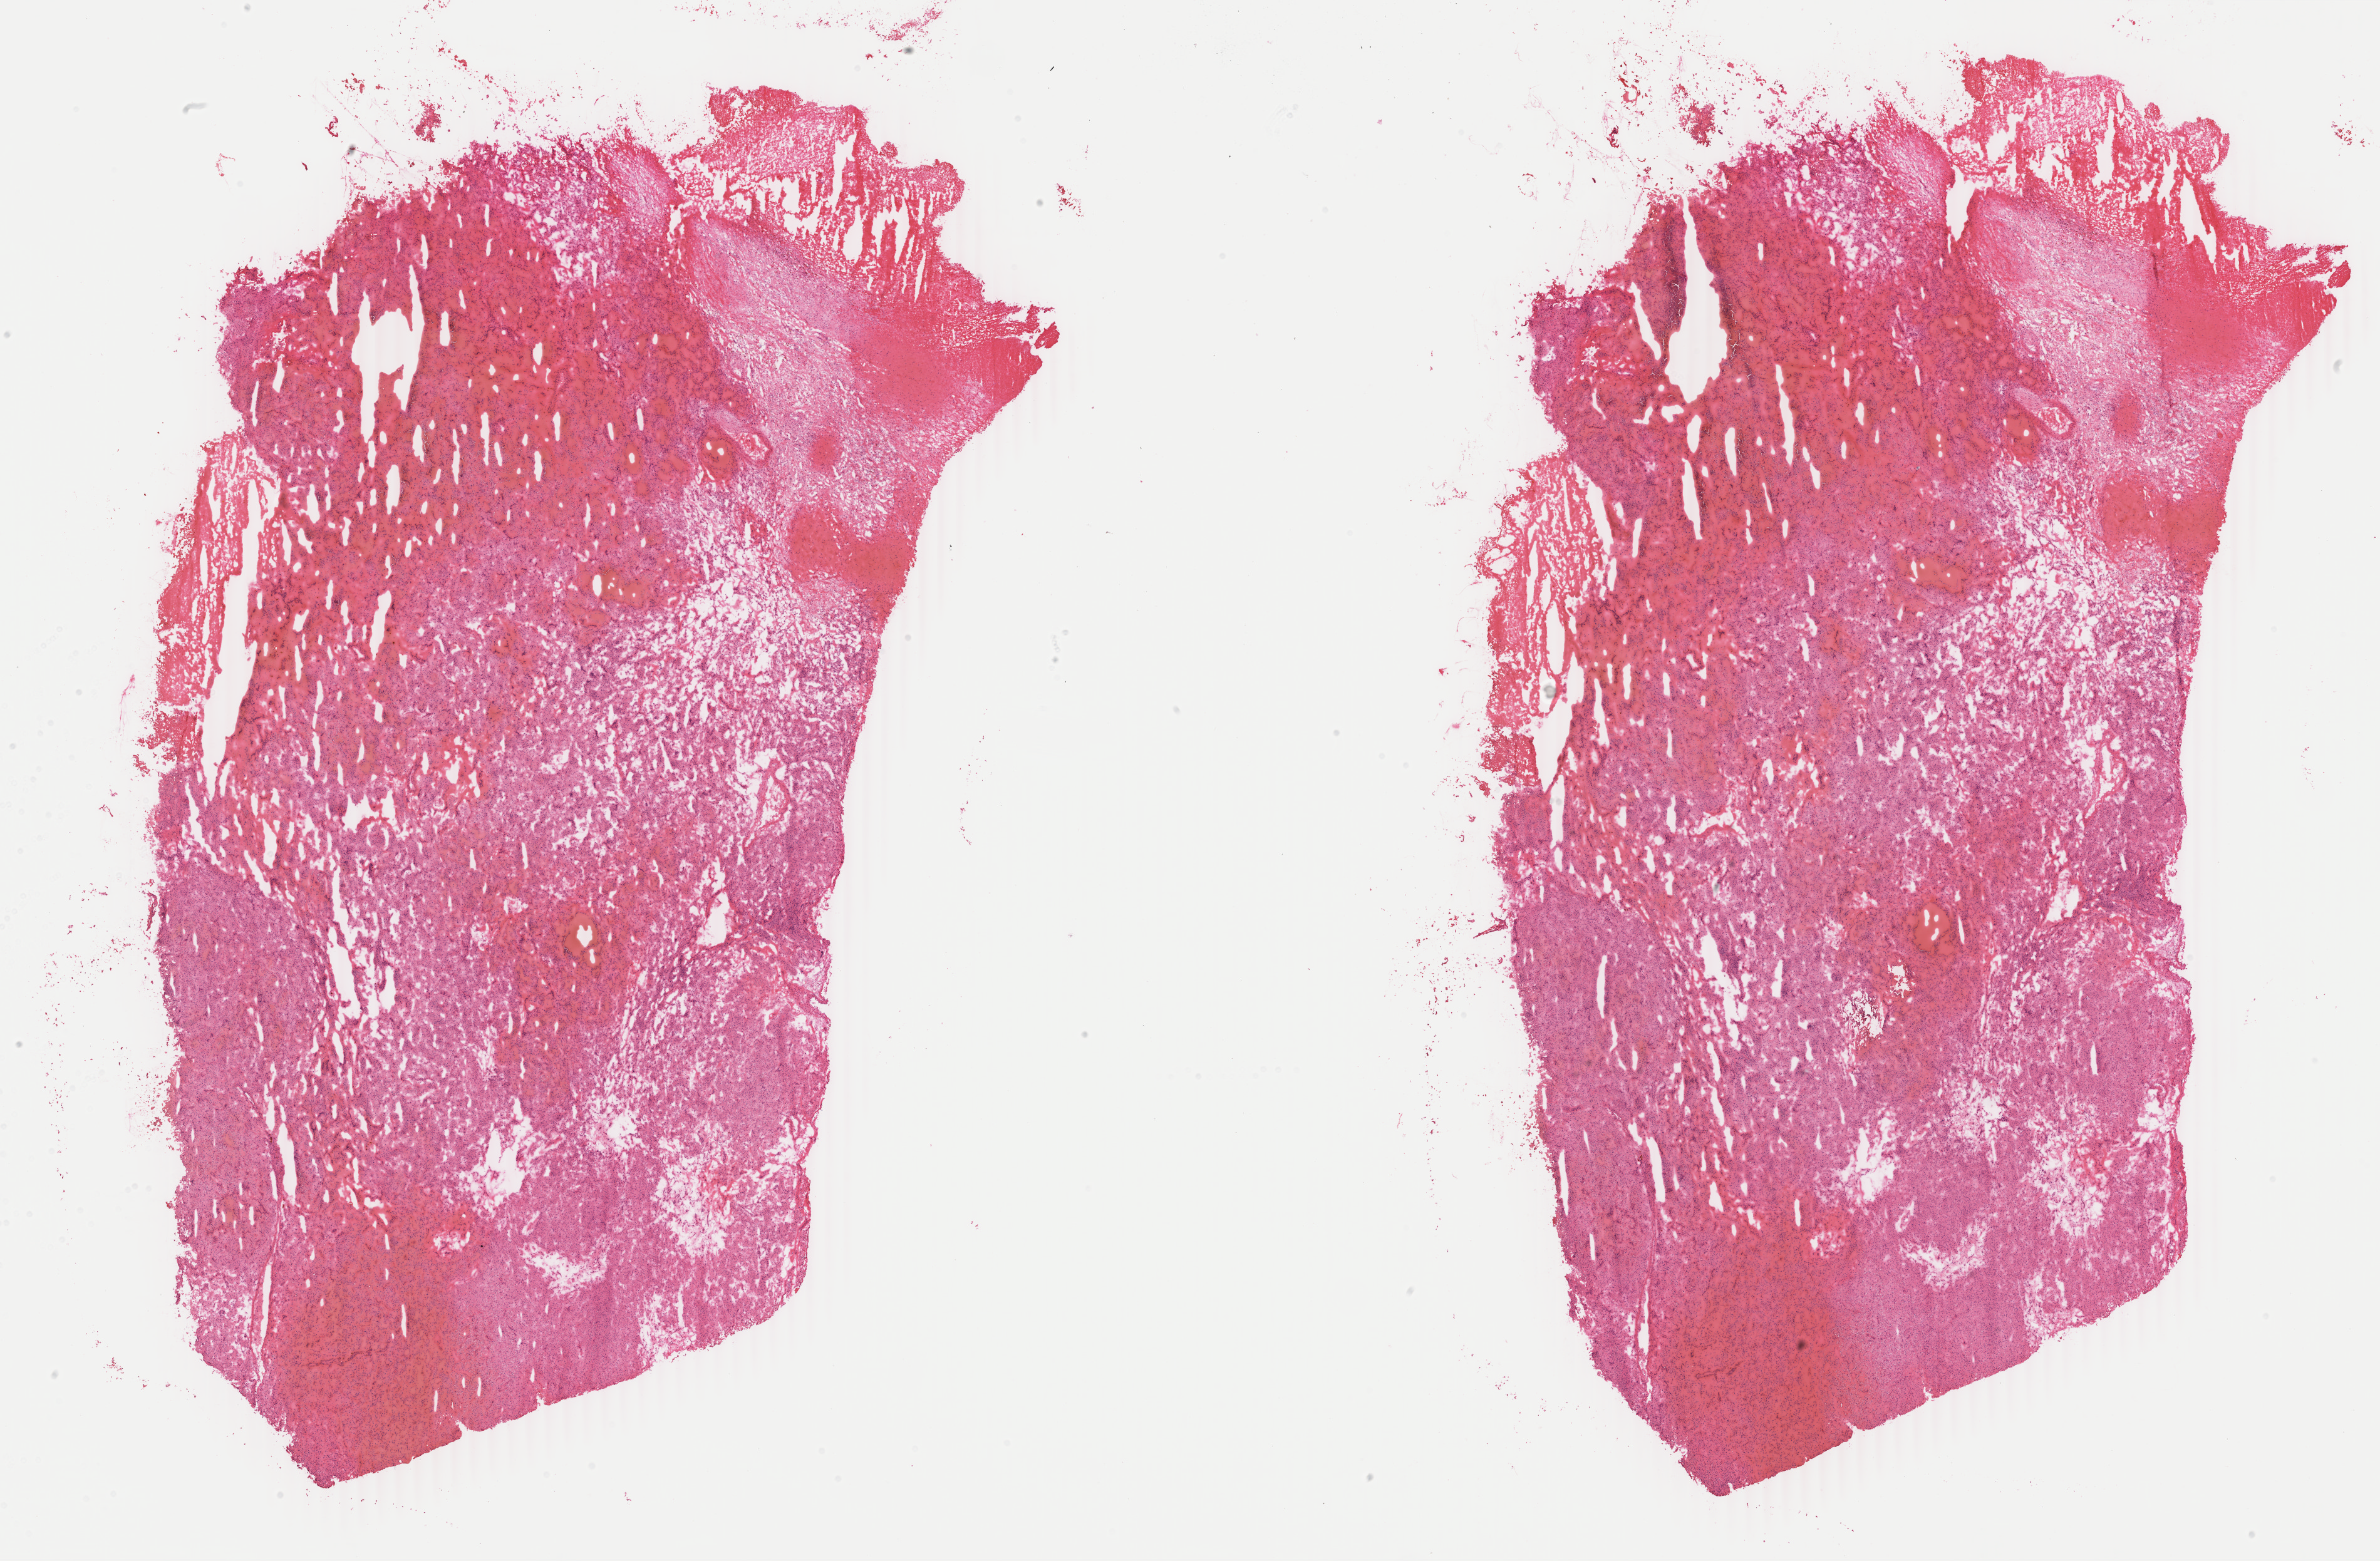
Digitized Hematoxylin and eosin (H&E) stained tissue section (whole slide), whole scanned area (about 30.2 x 19.8 mm, acquisition: 40x scan) shown as a low-resolution overview; frozen section; primary tumour sample from the kidney. Patient: male, age at initial diagnosis 55 years. Pathologist review of this section (percent, as recorded): tumour cells 70%, tumour nuclei 70%, normal cells 0%, stromal cells 30%, necrosis 0%. Infiltration values recorded for this section: lymphocyte infiltration 2%, monocyte infiltration 1%, neutrophil infiltration 1%.
- pathologic diagnosis: Renal cell carcinoma, chromophobe type
- AJCC pathologic stage: I (7th edition)
- laterality: right